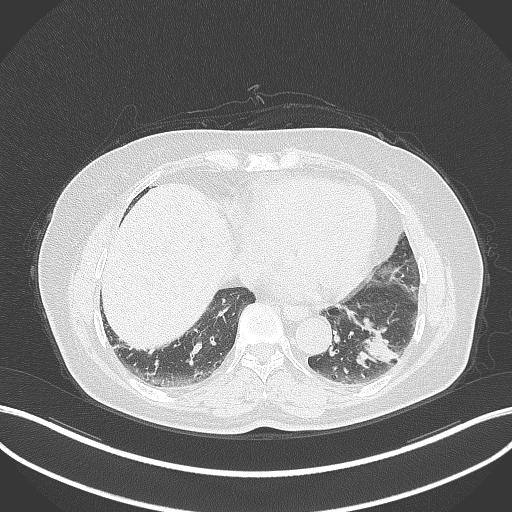
Chest CT, one axial slice; reconstruction kernel B70f; 120 kVp; lung window (W 1500 / L -600 HU); 1 mm slice thickness; 512 × 512 image matrix, field of view 400 × 400 mm. Patient: female, 59 years. Case-level facts recorded for this patient, not image findings: clinical TNM (as recorded): T2a N0 M0; histopathological grade: G2-3.
Annotated regions visible in this slice (bounding box drawn by a radiologist):
- lung tumour (recorded histology: adenocarcinoma): bounding box <349,314,401,373> (left, top, right, bottom; pixels)